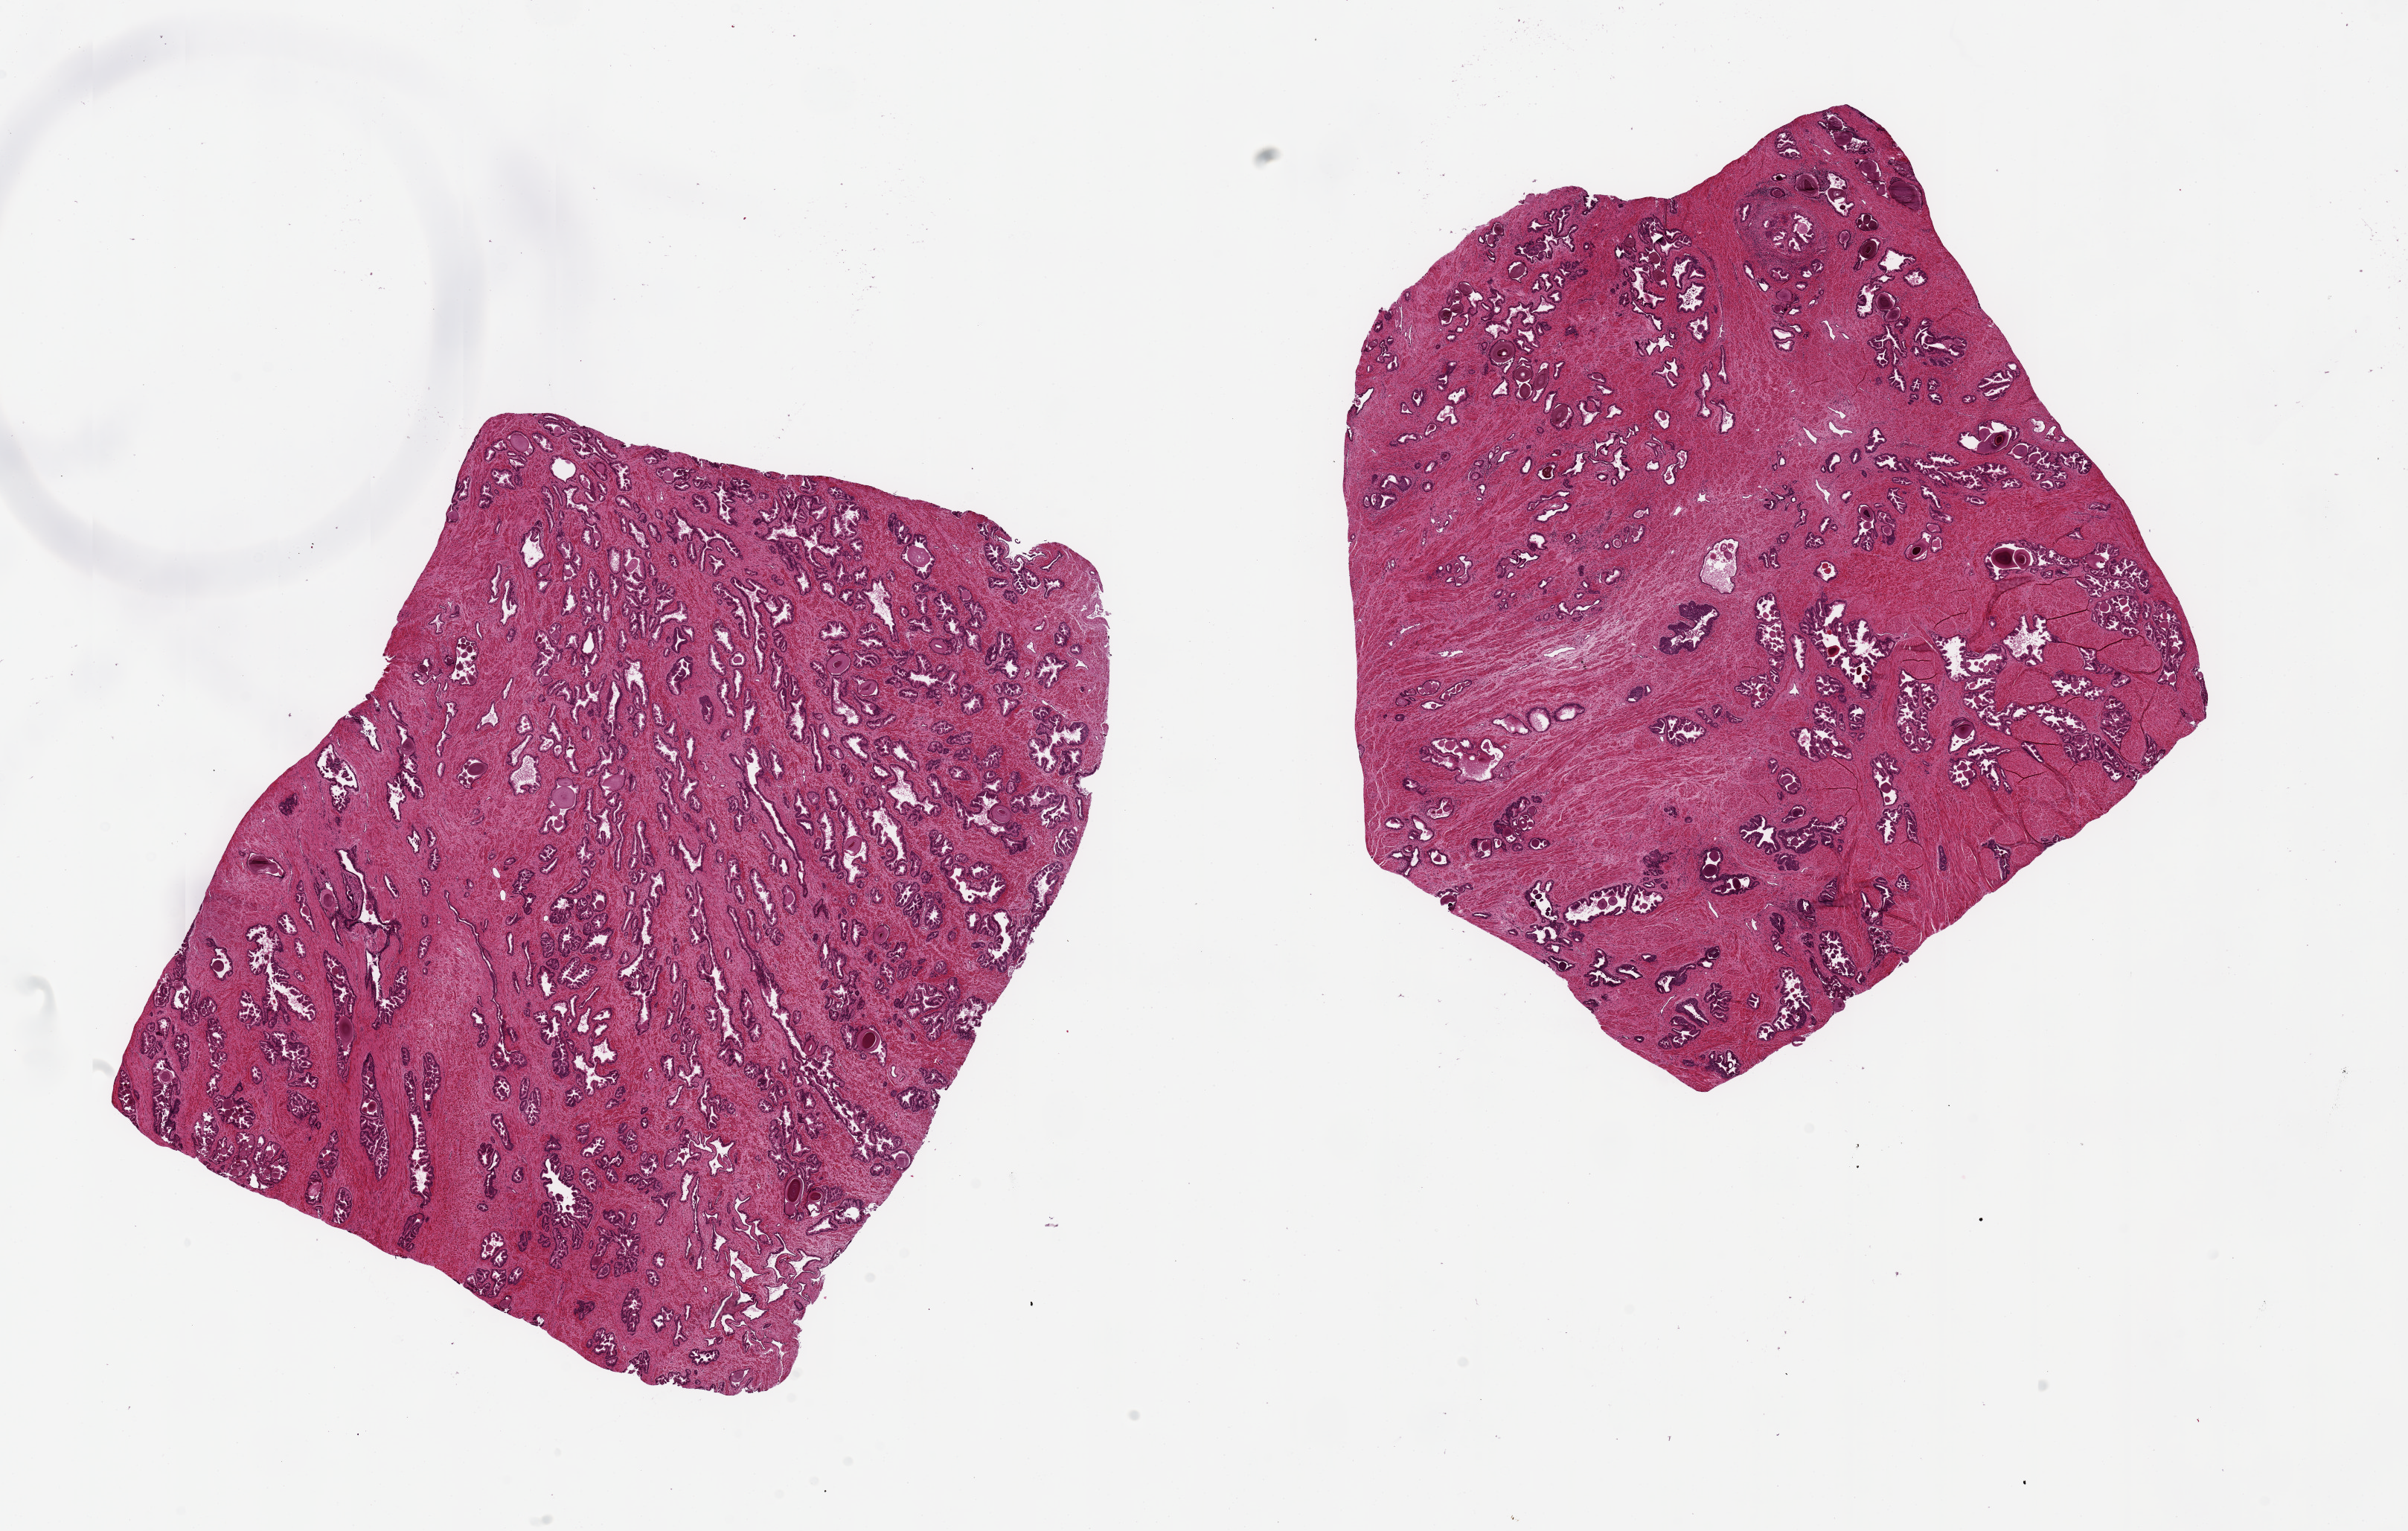
Whole-slide image, hematoxylin and eosin (H&E) stain — a low-resolution overview of the entire scanned area, about 25.6 x 16.3 mm (slide scanned at 20x). PAXgene-fixed, paraffin-embedded tissue. Target tissue: prostate. Tissue donor sample.
Reviewer comment on this tissue sample: 2 pieces, 10x8 & 9x9mm; glandular hyperplasia, fairly well preserved.